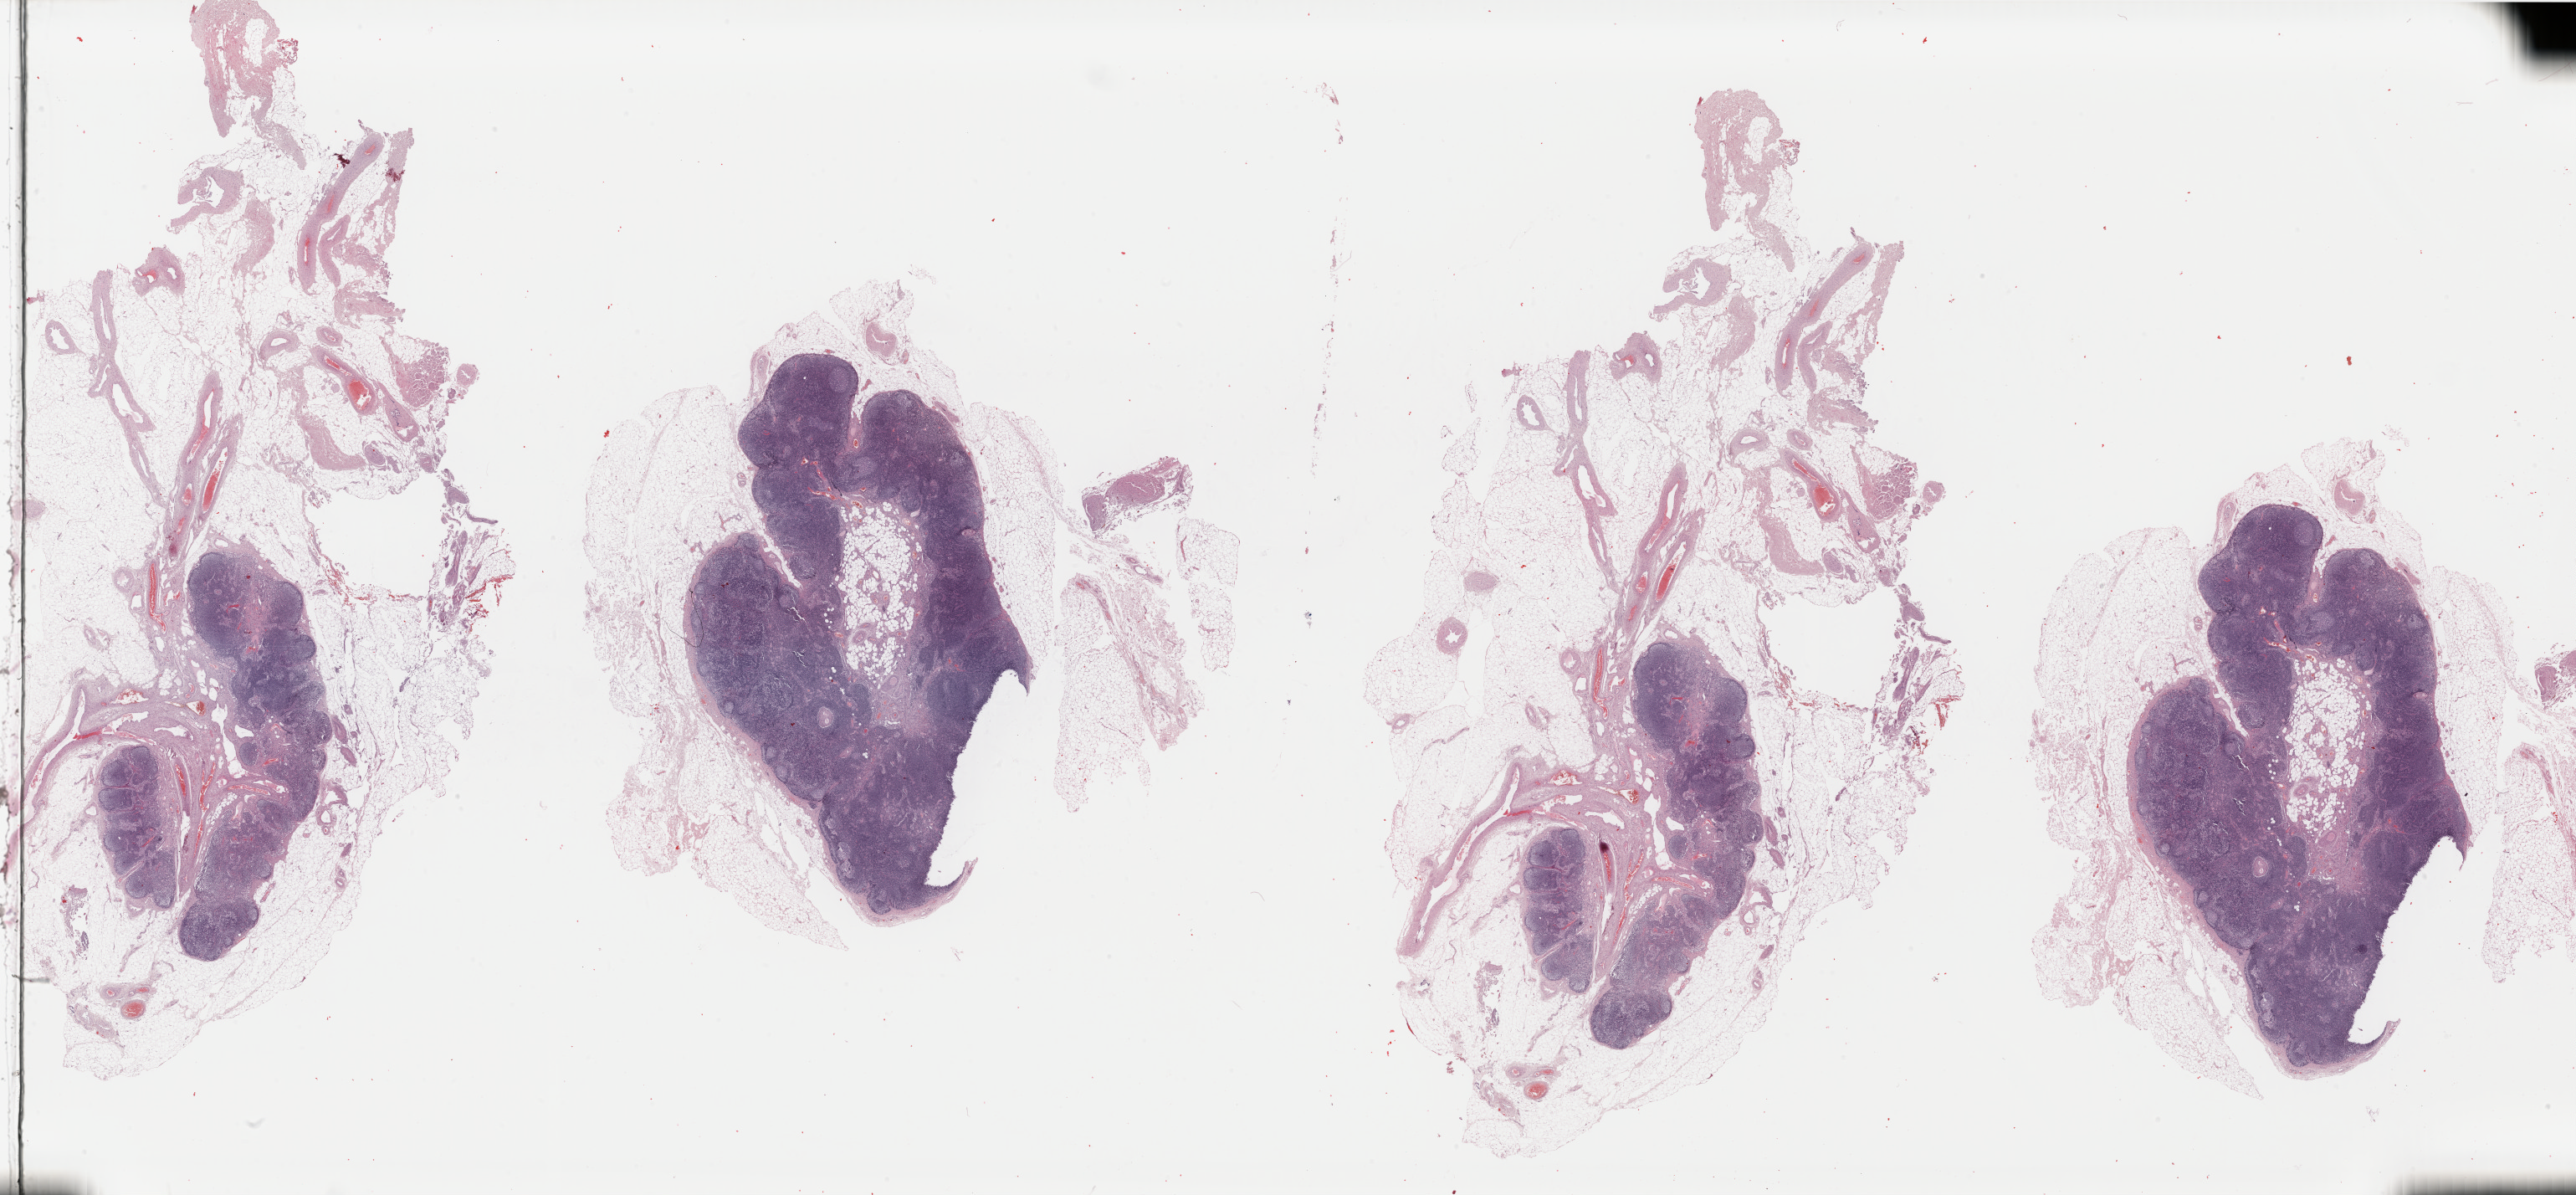
Digitized Hematoxylin and eosin (H&E) stained tissue section (whole slide), a low-resolution overview of the entire scanned area, about 48.9 x 22.7 mm; FFPE section; metastatic tumour sample, sampled site: lymph nodes of axilla or arm. Patient: female, age at initial diagnosis 39 years.
This section: metastatic tumour tissue. Patient diagnosis: Malignant melanoma, NOS.